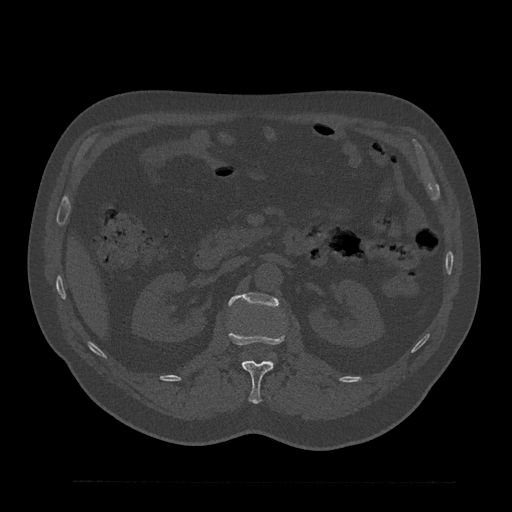
CT including the spine, one axial slice; position 144 of 797 along the scan axis; 120 kVp; bone window (W 1800 / L 400 HU); 0.5 mm slice thickness; 512 × 512 image matrix, field of view 430 × 430 mm. Patient: male, 61 years. From the clinical record (not read from this slice): primary cancer: prostate.
Structures marked on this image (semi-automatic segmentation, software-assisted and operator-edited):
- L1 vertebra: box from (x=229, y=331) to (x=285, y=404) px
- L2 vertebra: (x=228, y=293)–(x=279, y=306)